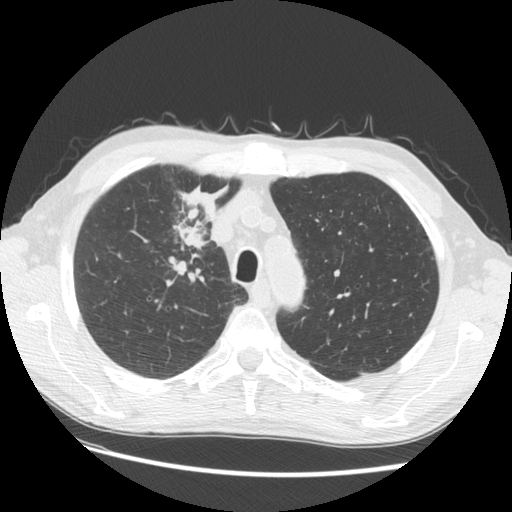
Low-dose screening chest CT, one axial slice; position 104 of 133 along the scan axis; reconstruction kernel STANDARD; lung window (W 1500 / L -600 HU); 2.5 mm slice thickness; 512 × 512 image matrix, field of view 360 × 360 mm.
Outlined on this slice (manually delineated by an expert):
- lesion 1 (tumor, hilum of right lung): bounding box (x1, y1, x2, y2) in pixels: (172, 182, 229, 250)